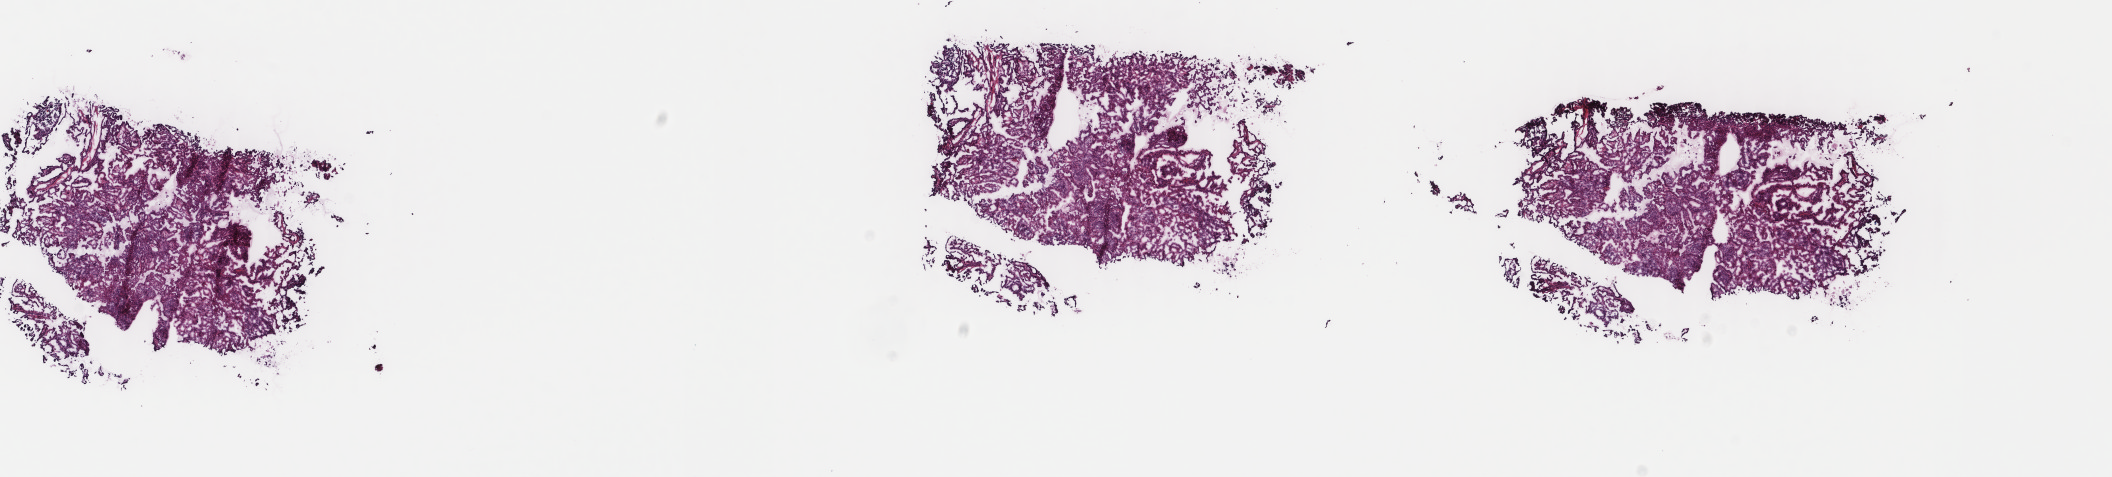
Whole-slide histology image, H&E-stained, a low-resolution overview of the entire scanned area, about 16.8 x 3.8 mm; frozen section; primary tumour sample from the thyroid. Patient: female, age at initial diagnosis 27 years. Pathologist review of this section (percent, as recorded): tumour cells 100%, tumour nuclei 95%, normal cells 0%, stromal cells 0%, necrosis 0%. Inflammatory infiltration, as recorded: lymphocyte infiltration 0%, monocyte infiltration 0%, neutrophil infiltration 0%.
Histologic diagnosis: Papillary adenocarcinoma, NOS (thyroid gland). AJCC pathologic stage: I.